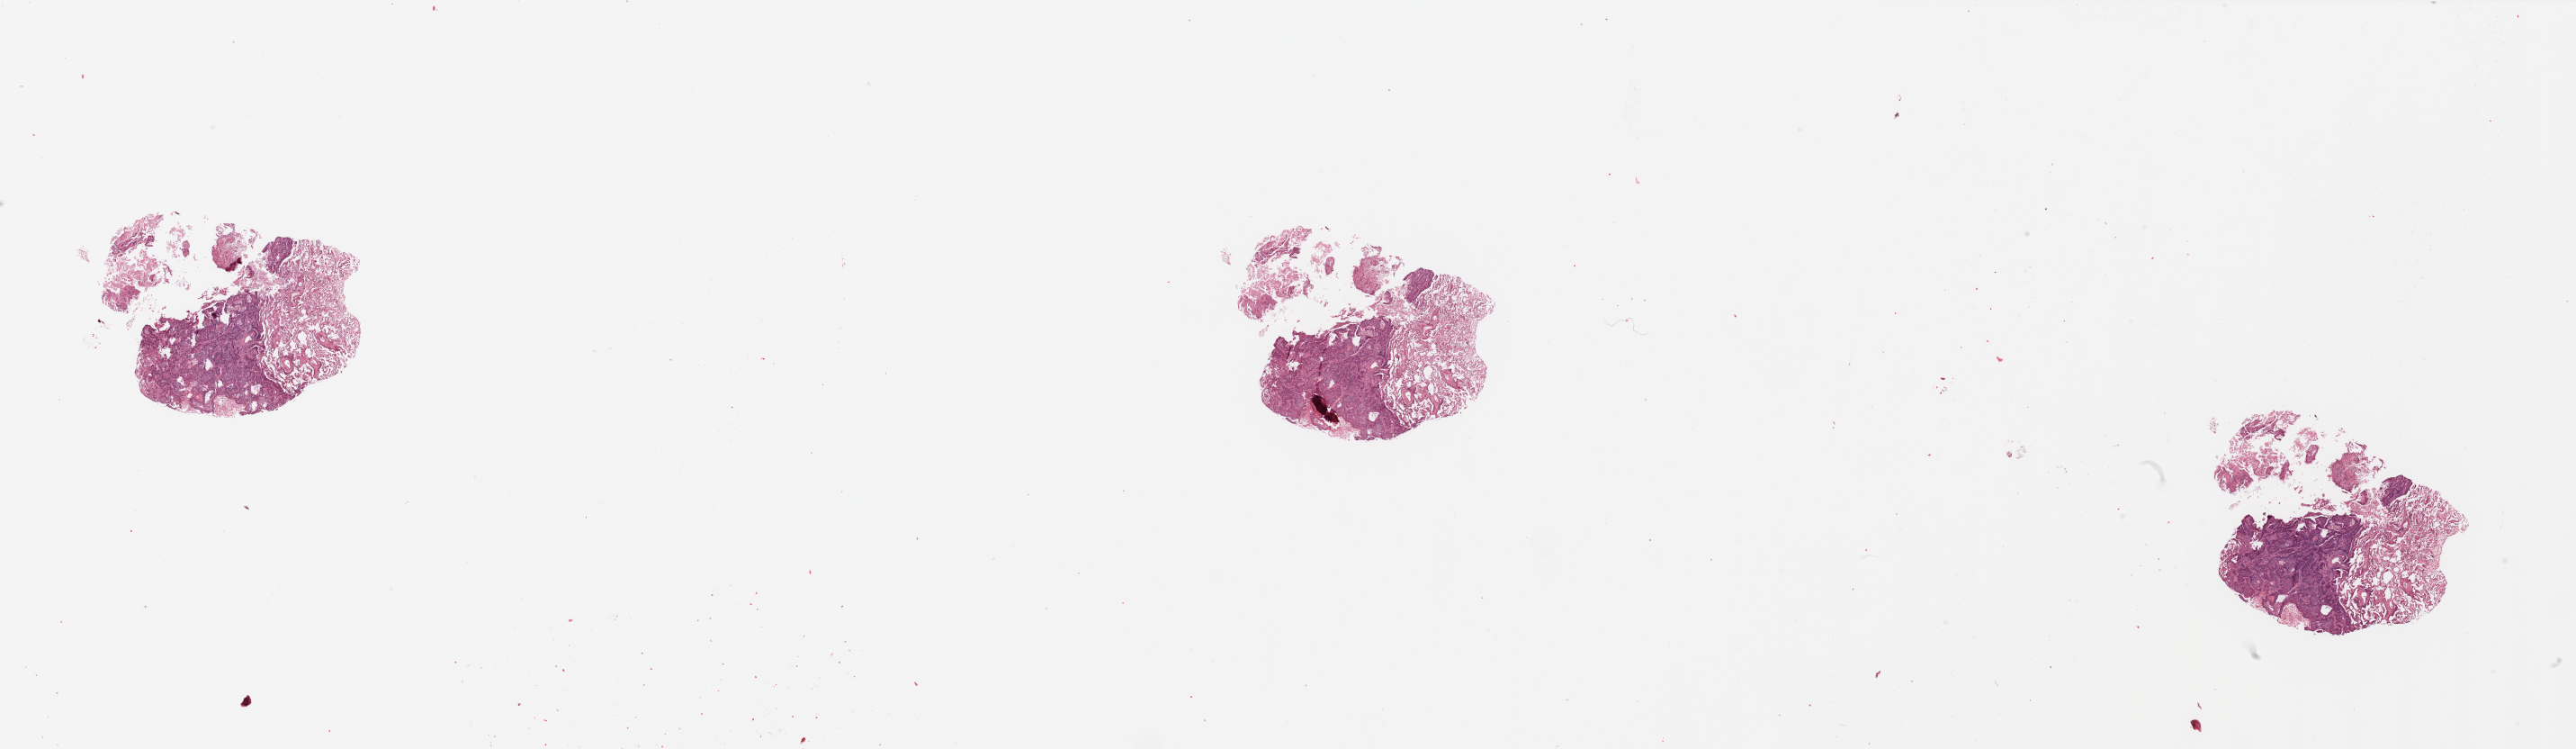
Digitized Hematoxylin and eosin (H&E) stained tissue section (whole slide), a low-resolution overview of the entire scanned area, about 45.3 x 13.2 mm (slide scanned at 20x). Tumour tissue sample, sampled site: lung. Patient: female, age 58 years. Histologic grade: G2 (moderately differentiated). Pathologist review of this section (percent, as recorded): tumour nuclei 65%, necrosis 10%.
Diagnosis: Squamous cell carcinoma, NOS. Primary tumour site (as recorded): left lower lobe. AJCC pathologic stage: III.